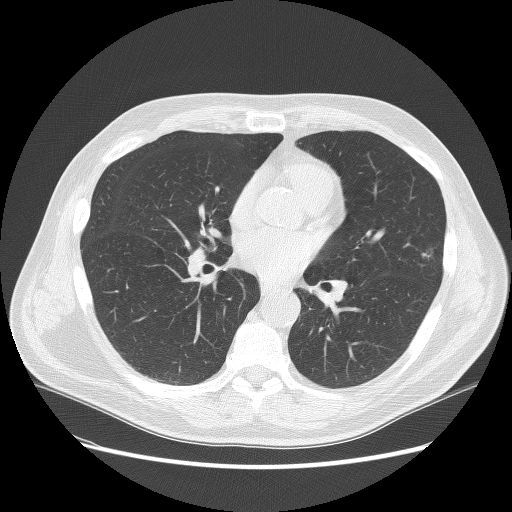
Low-dose screening chest CT, axial slice; second screening round (one year after baseline); lung window (W 1500 / L -600 HU); 2.5 mm slice thickness; lung (sharp) reconstruction kernel (BONE); slice 62 of 138 in the series; 512 × 512 image matrix. Male participant, aged 67 years at enrolment. Former smoker at enrolment.
Lesion marked by an expert reader, bounding box (x1, y1, x2, y2) in pixels: (400, 237, 454, 288). The exam's reader record, not a measurement of the box and not confirmed to be the same lesion: non-calcified nodule or mass ≥4 mm, left upper lobe, 10 × 6 mm, soft tissue attenuation, pre-existing on the prior screen: yes; interval growth: no. Participant outcome: lung cancer diagnosed 393 days after this screen (after the third annual screen) — squamous cell carcinoma, NOS, left upper lobe, moderately differentiated (G2), stage IB (AJCC 6th edition), 25 mm at pathology.